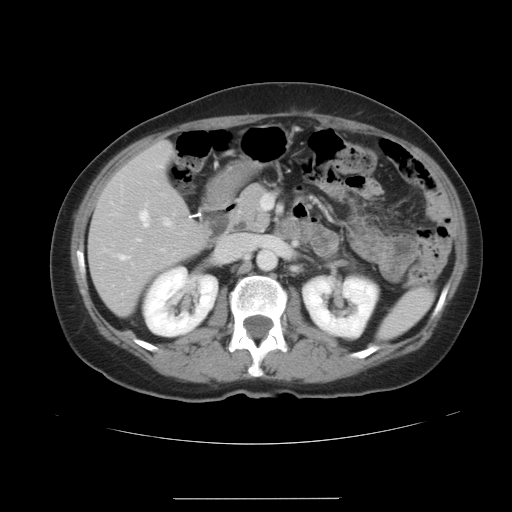
Contrast-enhanced abdominal CT, one axial slice; slice 18 of 41 in the series (ordered by position); soft-tissue window (W 400 / L 40 HU); 5 mm slice thickness; 512 × 512 image matrix, field of view 381 × 381 mm. Female patient, age 63 years. Case-level facts recorded for this patient, not image findings: diagnosis: colorectal cancer liver metastases, imaged before liver resection; multiple liver metastases: yes.
Annotated regions visible in this slice (expert manual segmentation):
- hepatic veins: bounding box <120,211,148,260> (left, top, right, bottom; pixels)
- liver: <89,142,207,315>
- planned liver remnant (the part of the liver to remain after resection): <89,143,207,315>
- portal vein (with intrahepatic branches): <164,221,170,225>
- liver metastasis: <130,164,135,169>